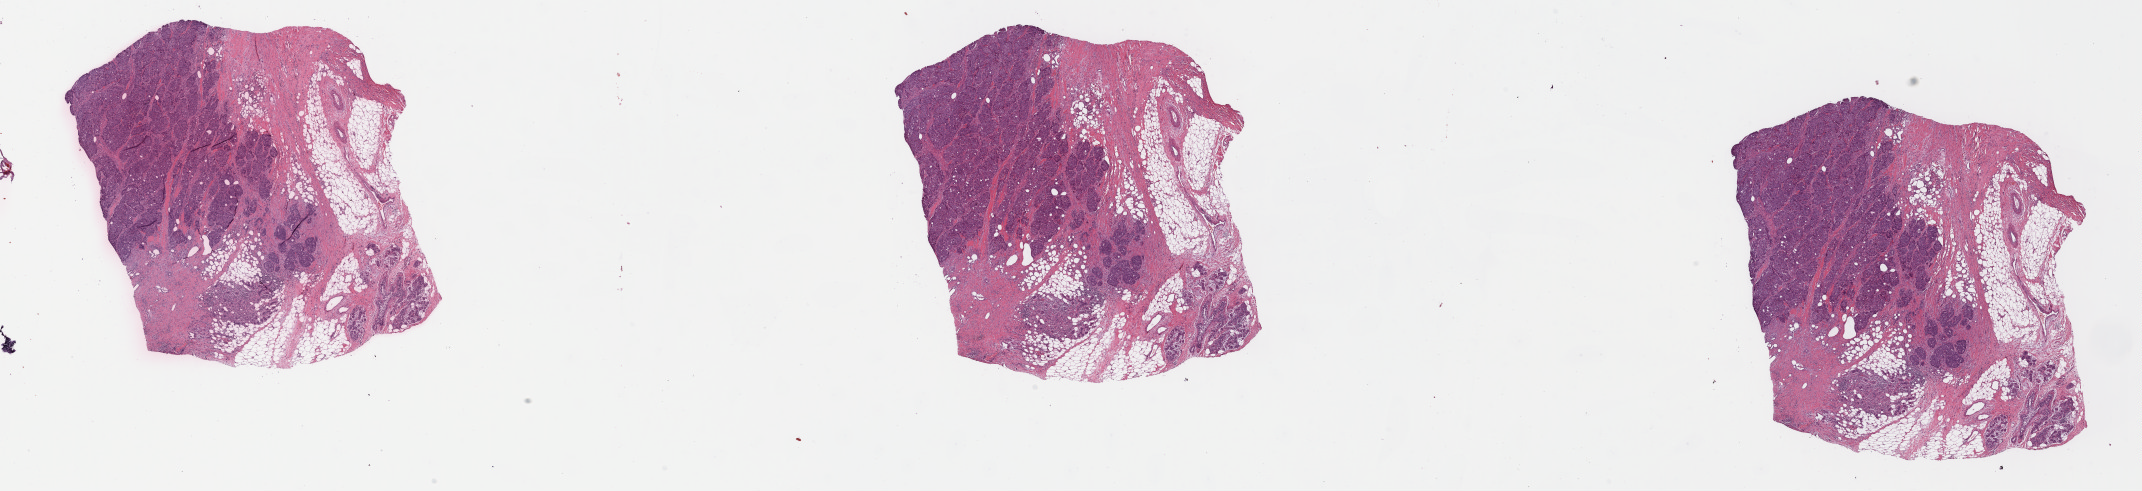
Whole-slide histology image, H&E-stained, shown as a low-resolution overview of the whole scanned area (about 33.7 x 7.7 mm, from a 40x scan); formalin-fixed paraffin-embedded (FFPE) diagnostic section; breast, primary tumour sample. Patient: female, age at initial diagnosis 48 years.
* lymph nodes positive (case pathology): 0 of 2 examined
* histologic diagnosis: Infiltrating duct carcinoma, NOS
* AJCC pathologic stage: IIA